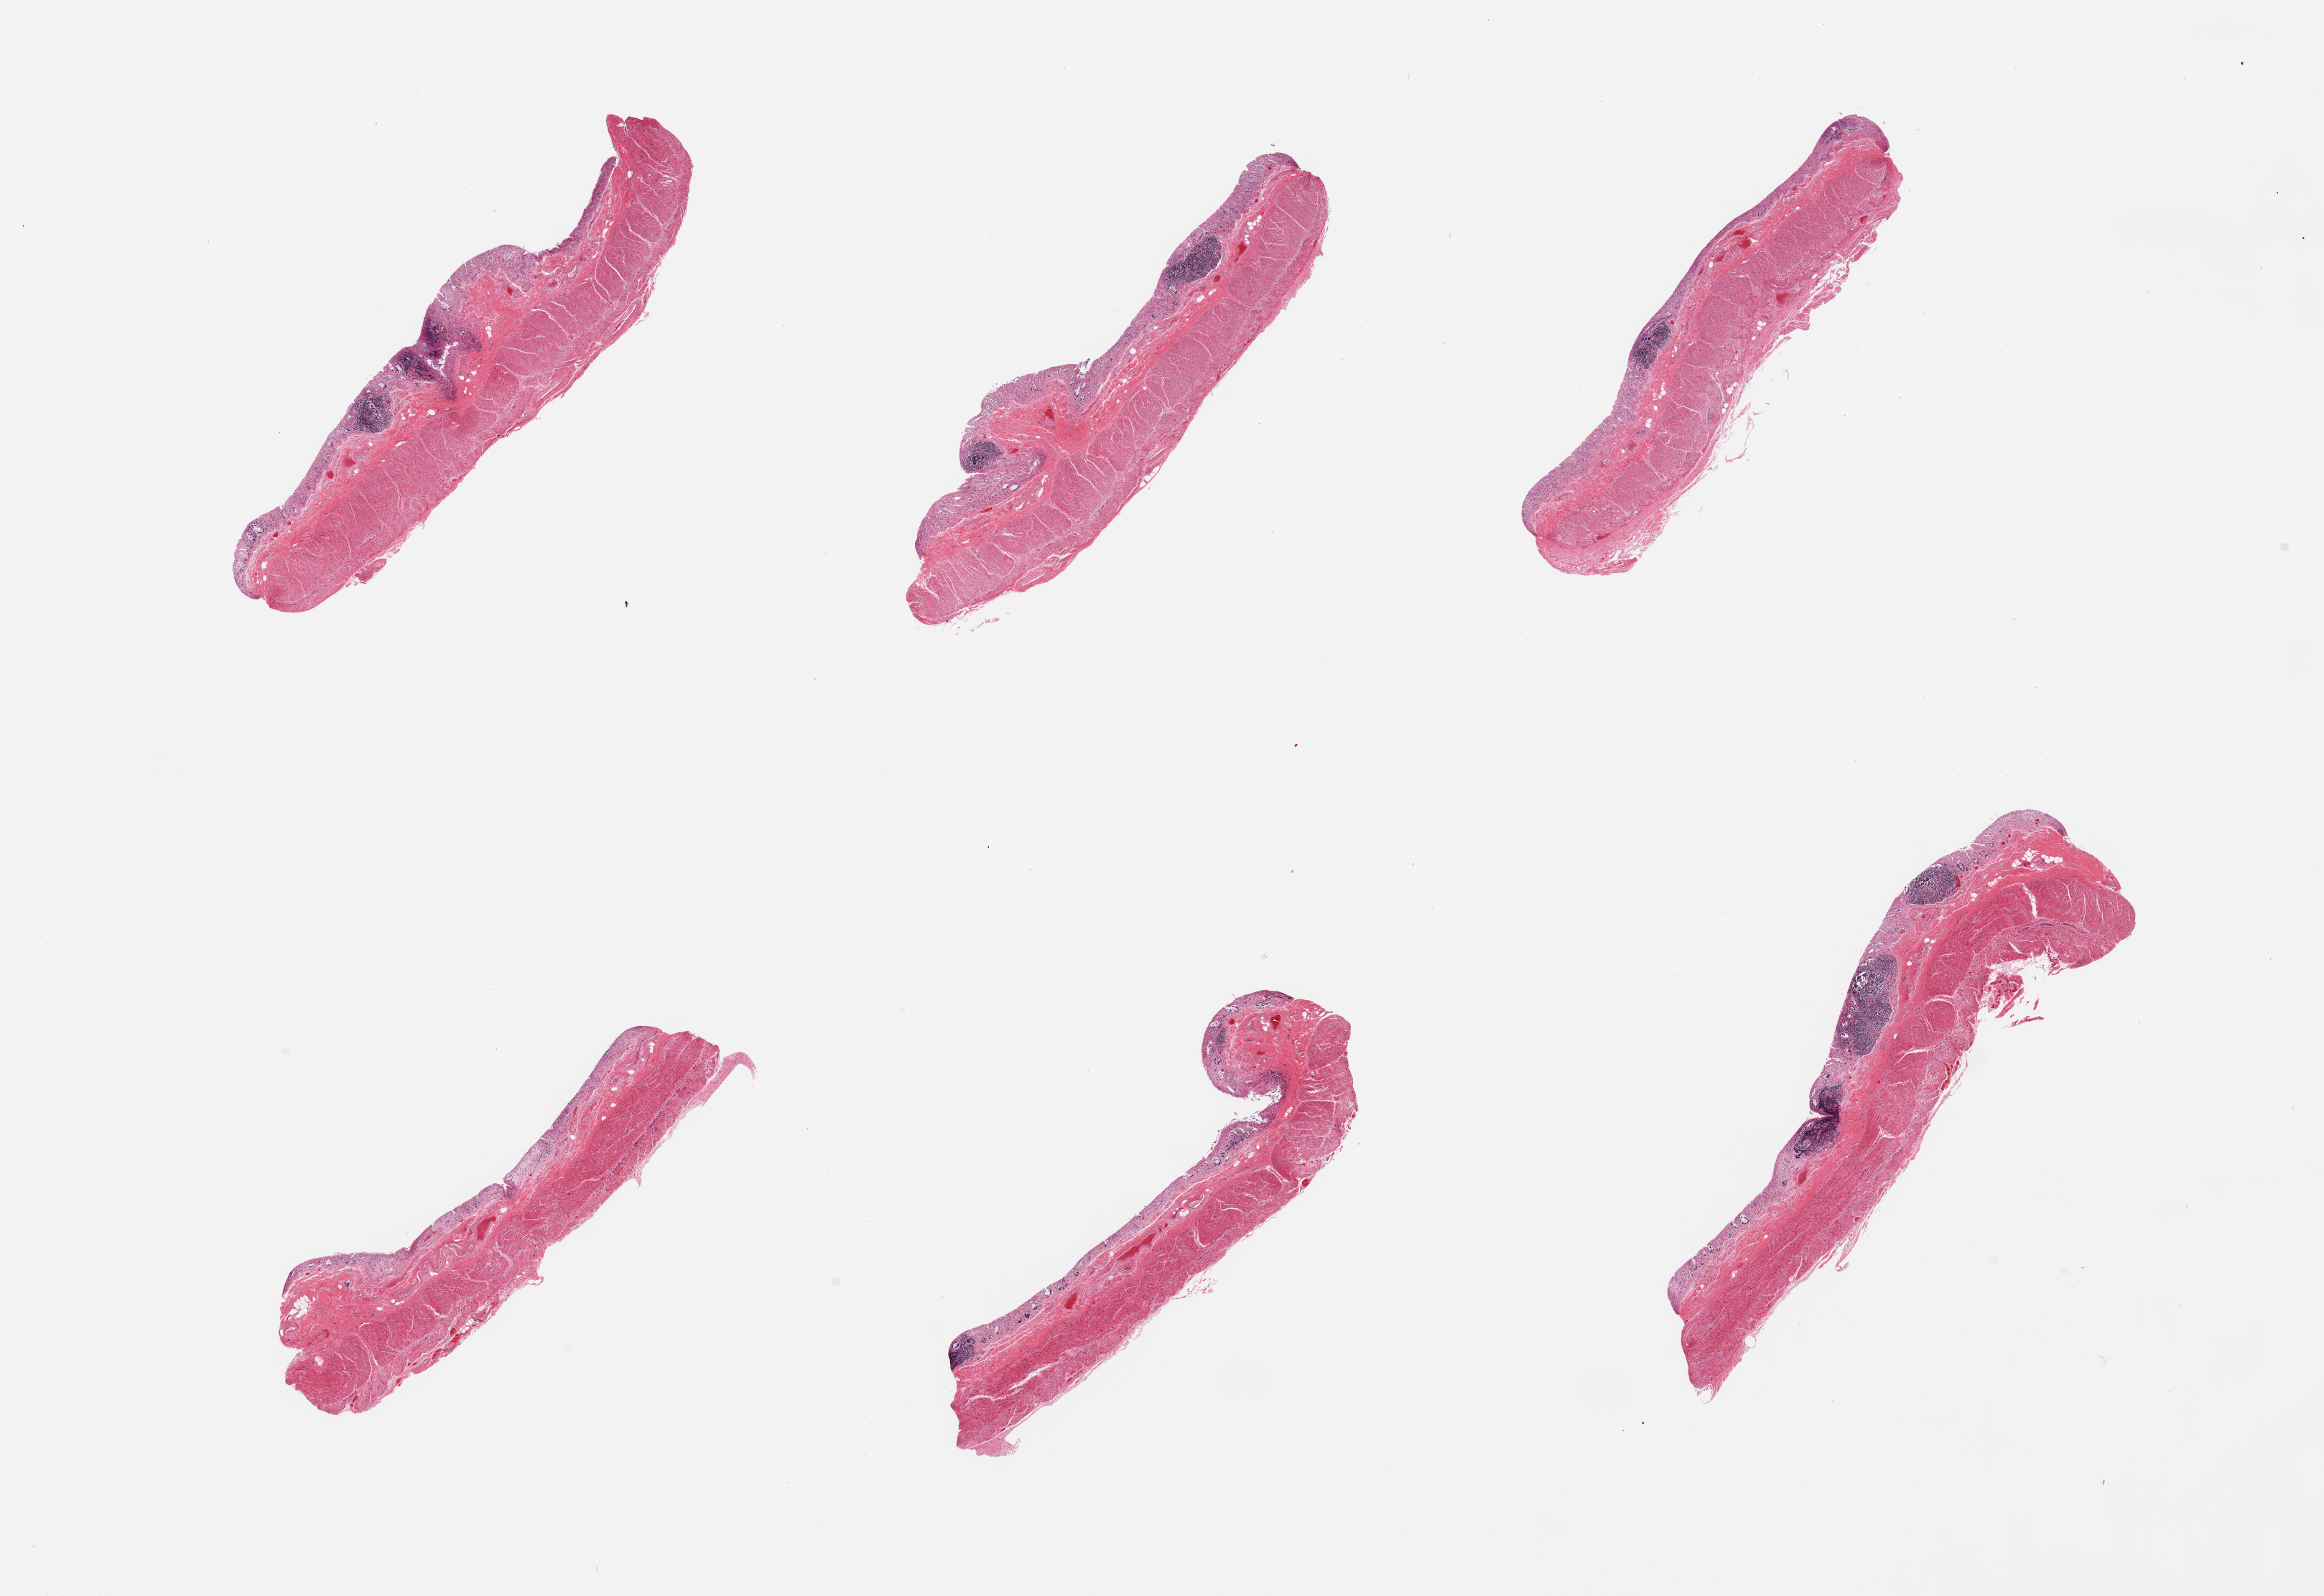
Hematoxylin and eosin (H&E) whole-slide image — low-resolution overview of the scanned area, about 25.6 x 17.6 mm (slide scanned at 20x); PAXgene-fixed, paraffin-embedded tissue; target tissue: transverse colon; donor tissue sample. Female donor.
Reviewer comment on this tissue sample: 6 pieces, mucosa completely autolyzed/sloughed.